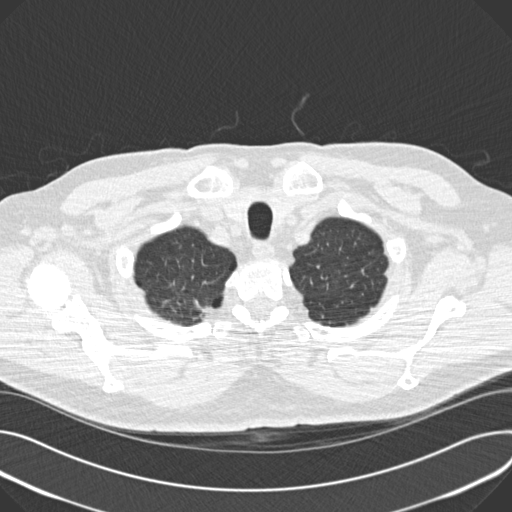
Low-dose screening chest CT, one axial slice; slice 162 of 180 in the series (ordered by position); reconstruction kernel B30f; lung window (W 1500 / L -600 HU); 512 × 512 image matrix, field of view 376 × 376 mm.
Annotated regions visible in this slice (outlined manually by an expert reader):
- lesion 1 (tumor, upper lobe of right lung): bounding box (x1, y1, x2, y2) in pixels: (202, 308, 214, 322)